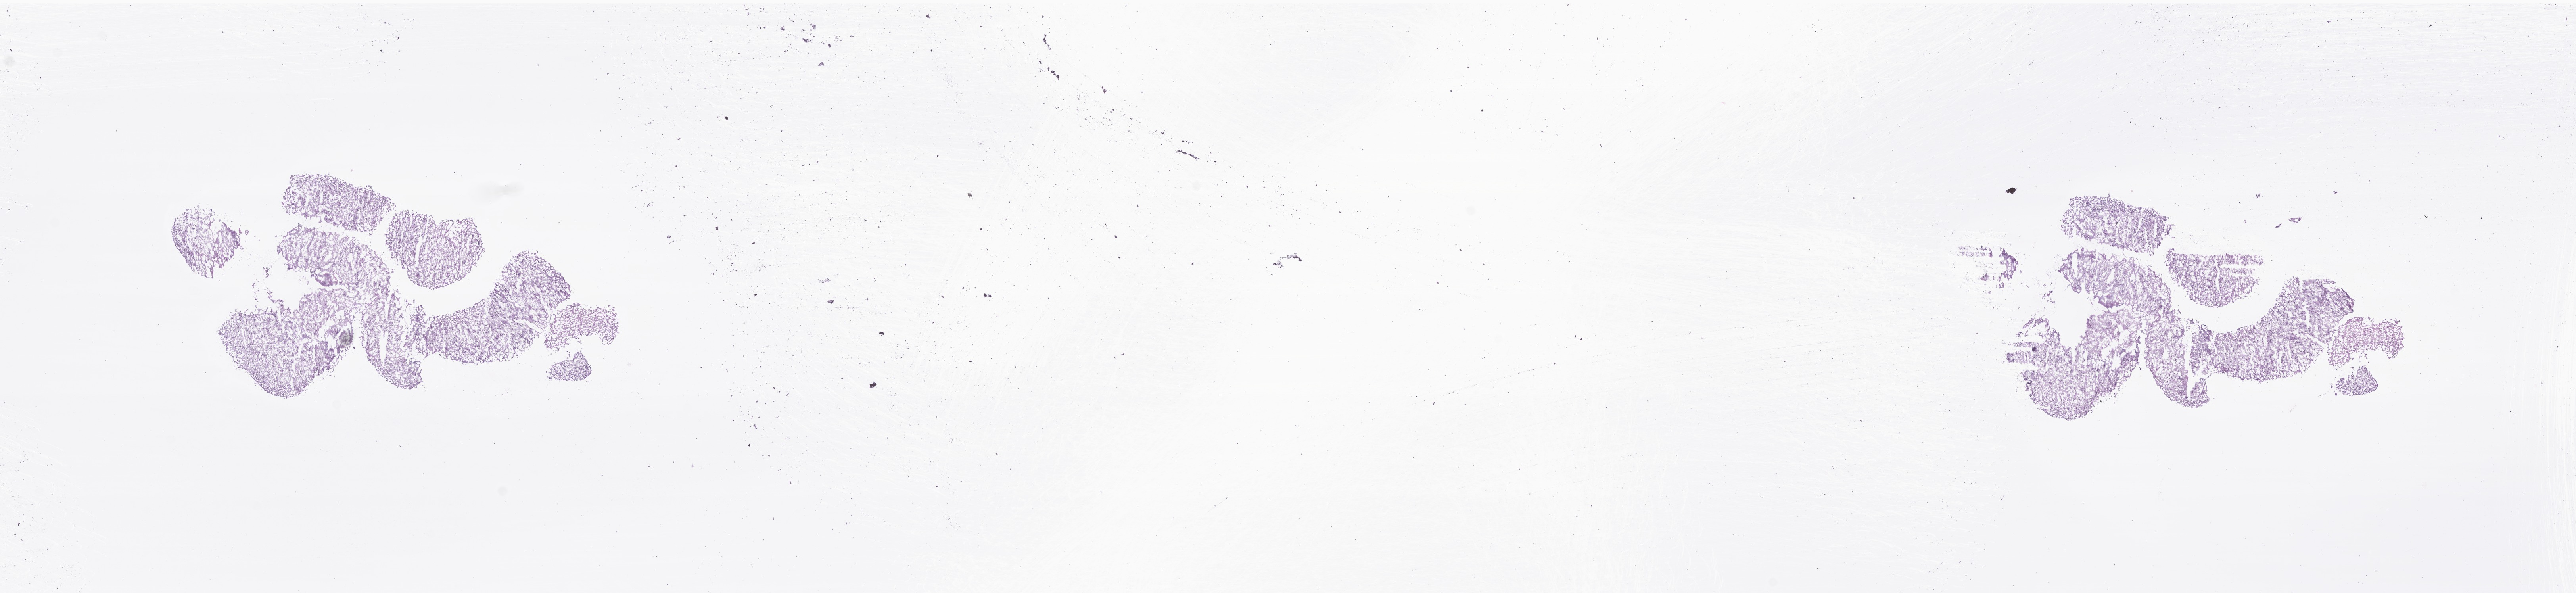
H&E whole-slide image of tumor tissue from the soft tissue of lower extremity, whole scanned area (about 27.4 x 6.3 mm) shown as a low-resolution overview. Cryosection (OCT / tissue freezing medium). Male patient, age 264 months (22 years).
Diagnosis: Hemangioendothelioma, malignant.